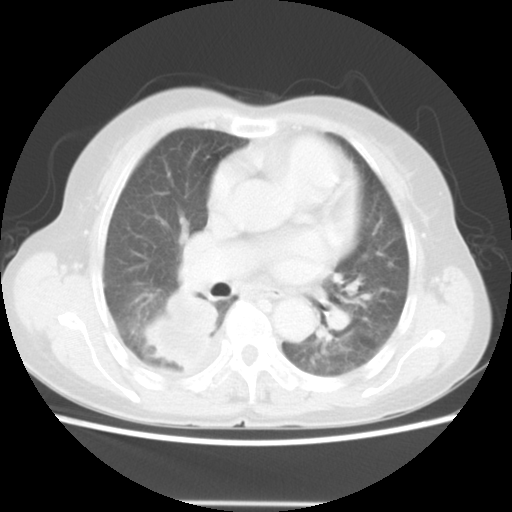
Chest CT, one axial slice. Slice 28 of 52 in the series (ordered by position). Reconstruction kernel STANDARD. 140 kVp. Lung window (W 1500 / L -600 HU). 5 mm slice thickness. 512 × 512 image matrix, field of view 337 × 337 mm. Female patient, age 67 years. From the clinical record (not read from this slice): clinical TNM (as recorded): T3 N1 M1.
Structures marked on this image (bounding box drawn by a radiologist):
- lung tumour (recorded histology: adenocarcinoma): bounding box [x1, y1, x2, y2] px = [145, 290, 220, 371]